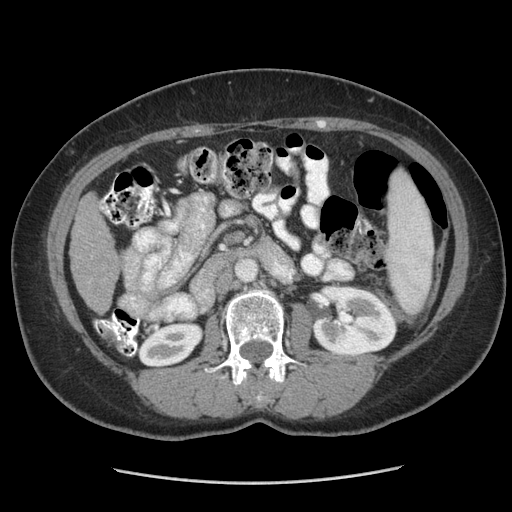
Contrast-enhanced abdominal CT (liver protocol), one axial slice. Reconstruction kernel STANDARD. 140 kVp. Soft-tissue window (W 400 / L 40 HU). 2.5 mm slice thickness. 512 × 512 image matrix, field of view 360 × 360 mm. From the clinical record (not read from this slice): diagnosis: hepatocellular carcinoma (patient treated with transarterial chemoembolisation; whether this scan precedes or follows treatment is not stated here); TNM stage (as recorded): Stage-I.
Annotated regions visible in this slice (semi-automatically segmented with operator editing):
- liver parenchyma outside the tumour (the mass and vessels are separate outlines, so this box may not span the whole liver): bounding box [x1, y1, x2, y2] px = [70, 194, 118, 312]